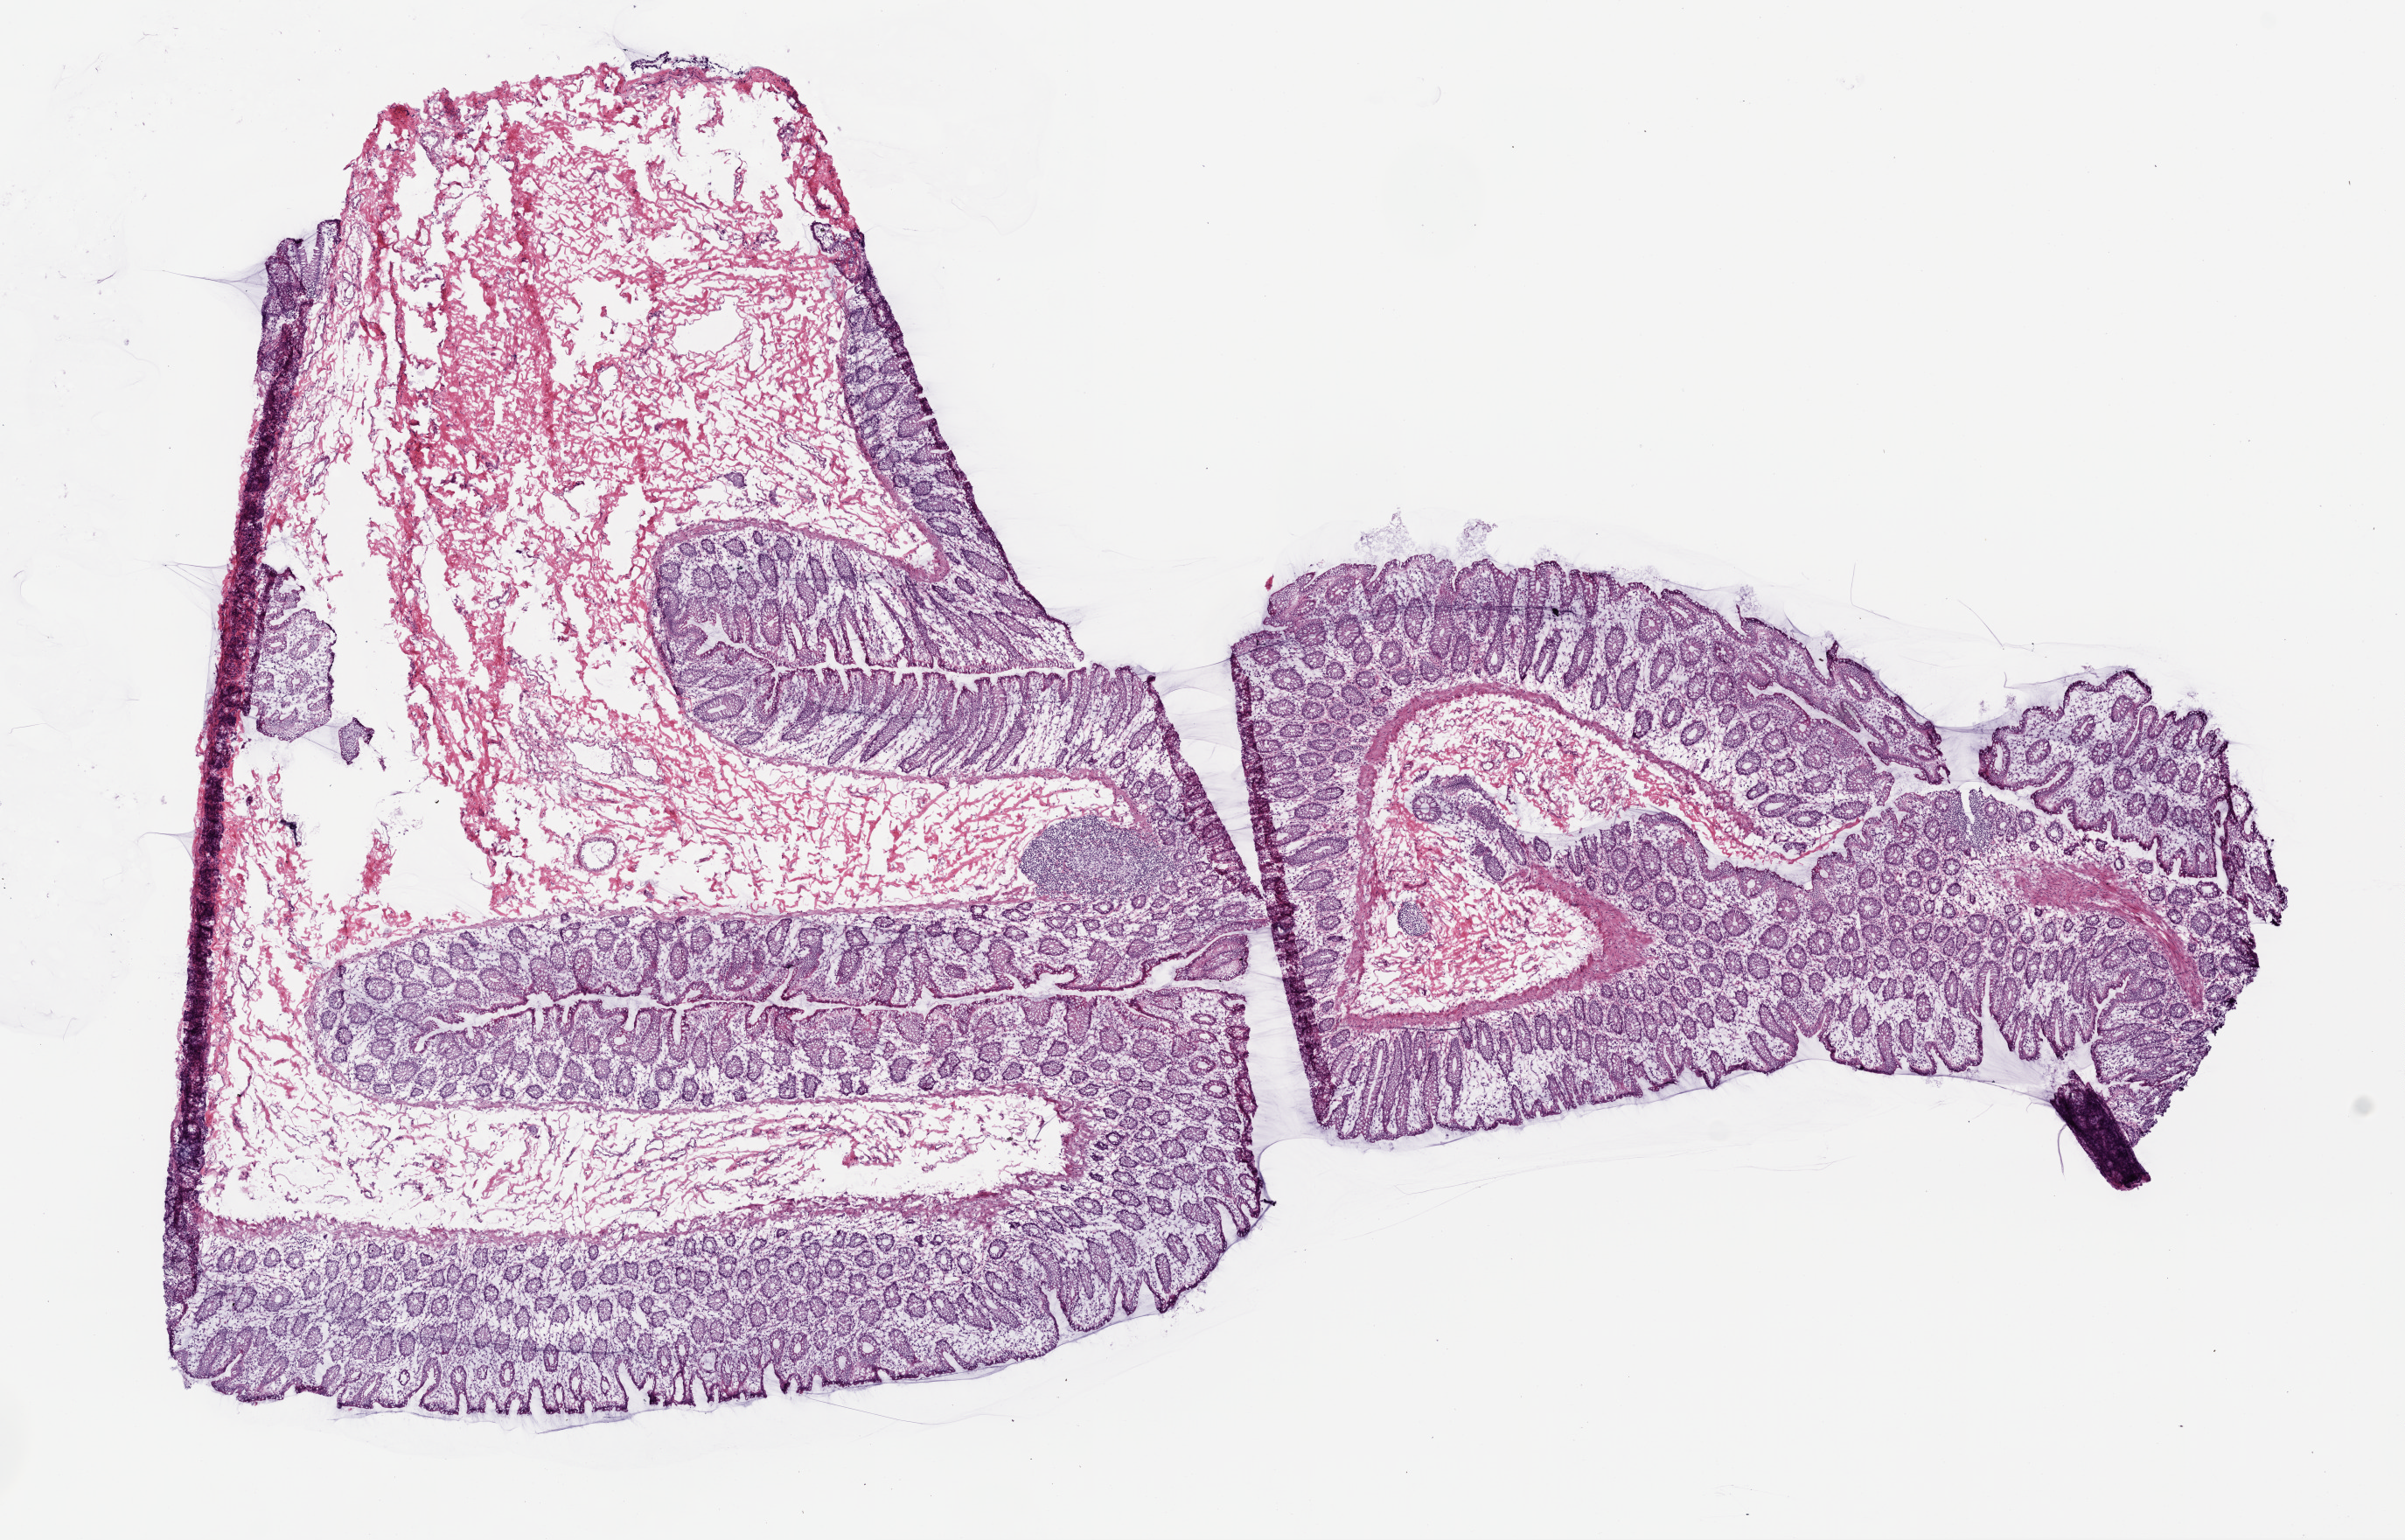
H&E whole-slide image, whole scanned area (about 11.0 x 7.1 mm, acquisition: 20x scan) shown as a low-resolution overview. Frozen section from the top of the tissue portion. Sample: solid tissue normal (non-tumour tissue), colon. Male, age 80 years at initial diagnosis.
- this section: solid tissue normal (non-tumour) sample from the same patient
- patient diagnosis: Adenocarcinoma, NOS (ascending colon)